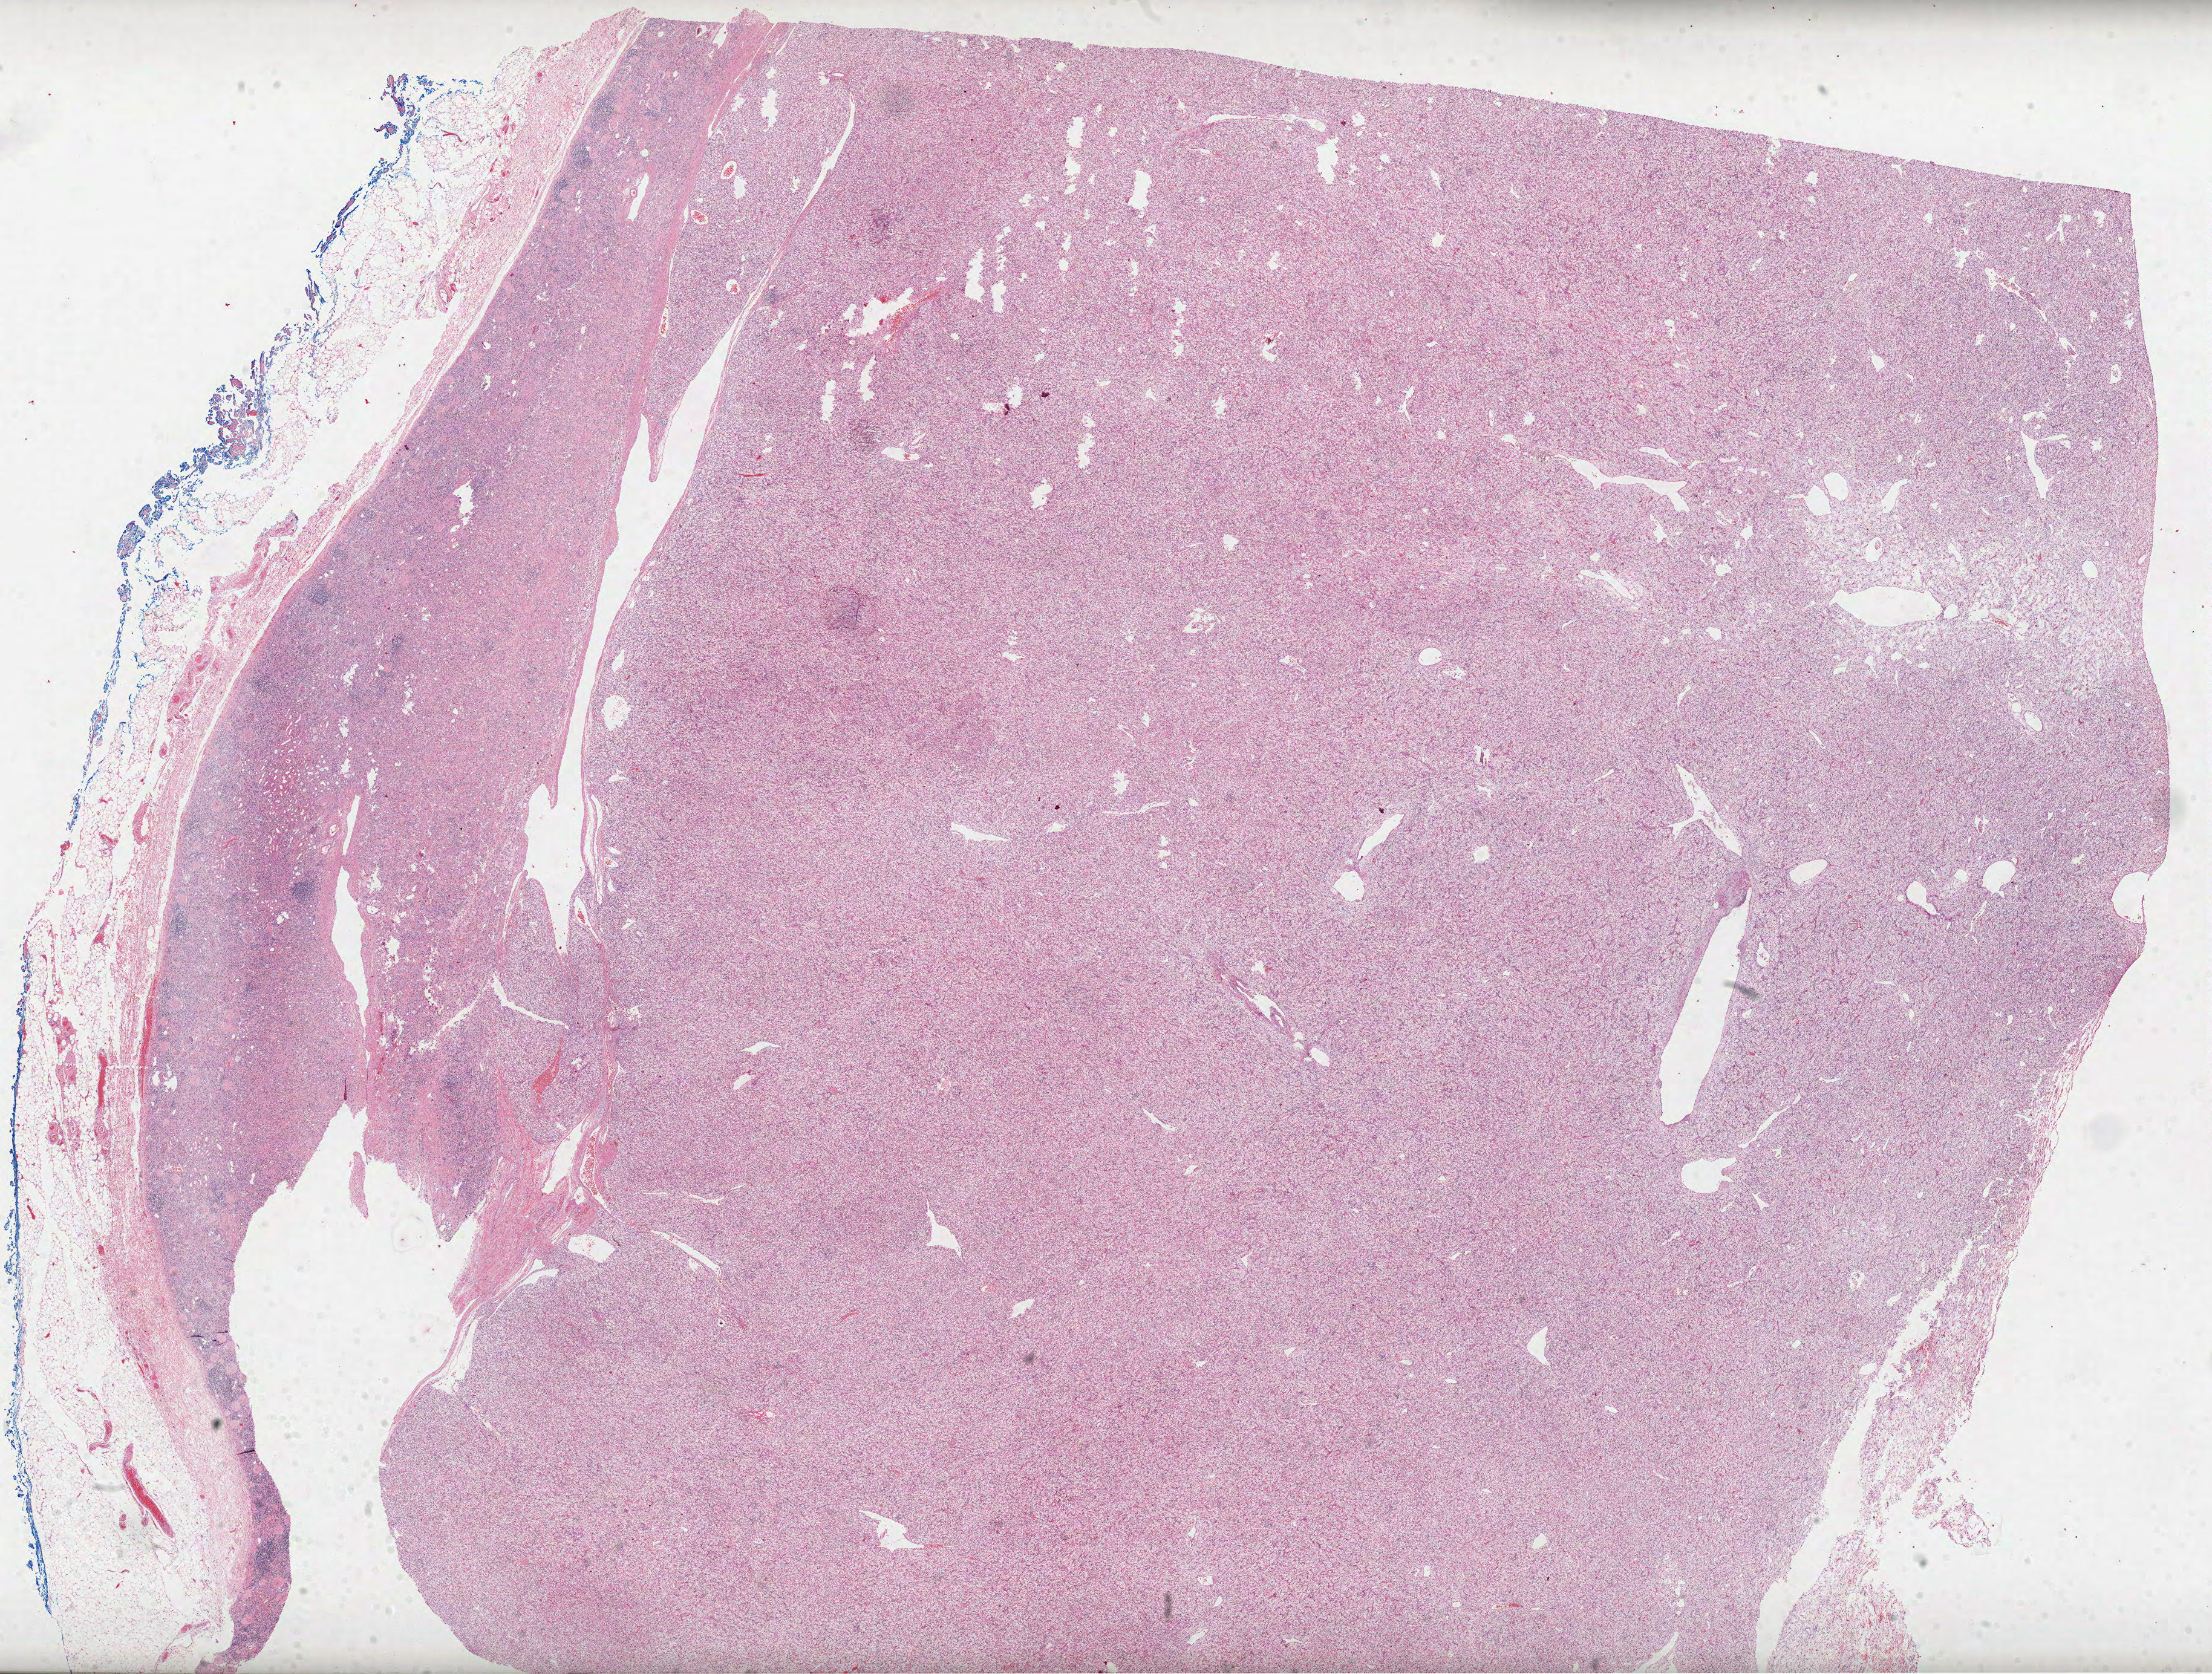
H&E-stained whole-slide image, shown as a low-resolution overview of the whole scanned area (about 29.5 x 22.3 mm), formalin-fixed paraffin-embedded (FFPE) diagnostic section, primary tumour sample from the kidney. Patient: male, age at initial diagnosis 52 years. Histologic grade: G2 (moderately differentiated).
• AJCC pathologic stage: IV (6th edition)
• histologic diagnosis: Clear cell adenocarcinoma, NOS